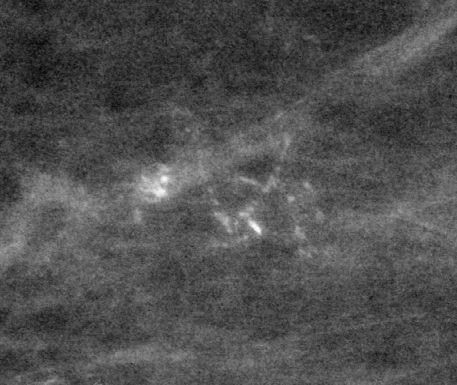
Region of interest cut from a scanned film mammogram (one marked finding), left breast, CC view.
Calcifications, morphology pleomorphic / fine linear branching, distribution clustered / linear; BI-RADS assessment category 5; subtlety rating 4 on a 1 (subtle) to 5 (obvious) scale; pathology (as recorded): malignant.